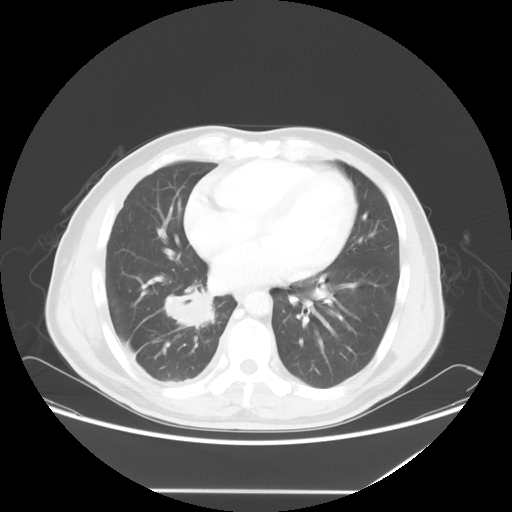
Chest CT, one axial slice. Position 24 of 60 along the scan axis. Lung window (W 1500 / L -600 HU). 5 mm slice thickness. 512 × 512 image matrix. Patient: male, 48 years. From the clinical record (not read from this slice): clinical TNM (as recorded): T3 N3 M1a.
Outlined on this slice (rectangle marked by the reading radiologist):
- lung tumour (recorded histology: squamous cell carcinoma): bounding box [x1, y1, x2, y2] px = [157, 280, 223, 332]